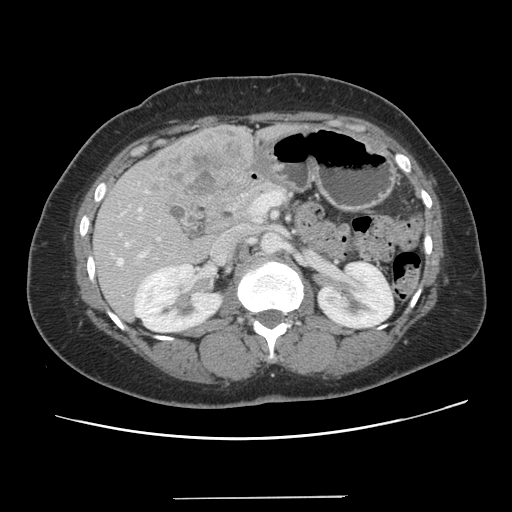
Contrast-enhanced abdominal CT, one axial slice; position 61 of 141 along the scan axis; intravenous contrast given; soft-tissue window (W 400 / L 40 HU); 2.5 mm slice thickness; 512 × 512 image matrix, field of view 366 × 366 mm. Female patient, age 53 years. Case-level facts recorded for this patient, not image findings: diagnosis: colorectal cancer liver metastases, imaged before liver resection; multiple liver metastases: no; largest metastasis: 14.5 cm; disease in both lobes: yes.
Annotated regions visible in this slice (outlined manually by an expert reader):
- hepatic veins: bounding box [x1, y1, x2, y2] px = [116, 242, 128, 264]
- liver: [93, 126, 254, 320]
- planned liver remnant (the part of the liver to remain after resection): [93, 214, 210, 320]
- portal vein (with intrahepatic branches): [138, 208, 158, 257]
- liver metastasis: [152, 128, 244, 197]